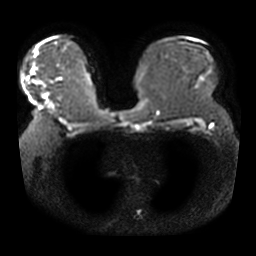
Breast MRI, one axial slice. Slice 25 of 42 in the series (ordered by position). Diffusion-weighted series; image 2 of 4 stored at this slice position (different b-values; order by instance number). 3 T. 5 mm slice thickness. 256 × 256 image matrix. Female patient.
Annotated regions visible in this slice (expert manual segmentation):
- tumour on diffusion-weighted imaging: bounding box <31,68,33,73> (left, top, right, bottom; pixels)